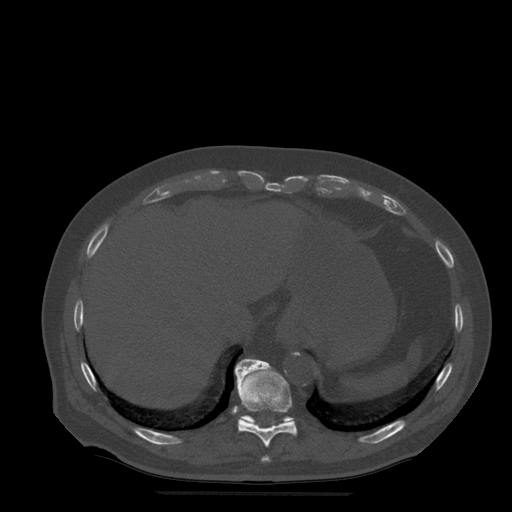
CT including the spine, one axial slice. Slice 263 of 522 in the series (ordered by position). Bone window (W 1800 / L 400 HU). 1.25 mm slice thickness. 512 × 512 image matrix, field of view 420 × 420 mm. Patient age 72 years. From the clinical record (not read from this slice): primary cancer: prostate.
Annotated regions visible in this slice (semi-automatically segmented with operator editing):
- T10 vertebra: bounding box (x1, y1, x2, y2) in pixels: (235, 359, 298, 448)
- T11 vertebra: (239, 359, 293, 425)
- T9 vertebra: (262, 456, 271, 462)